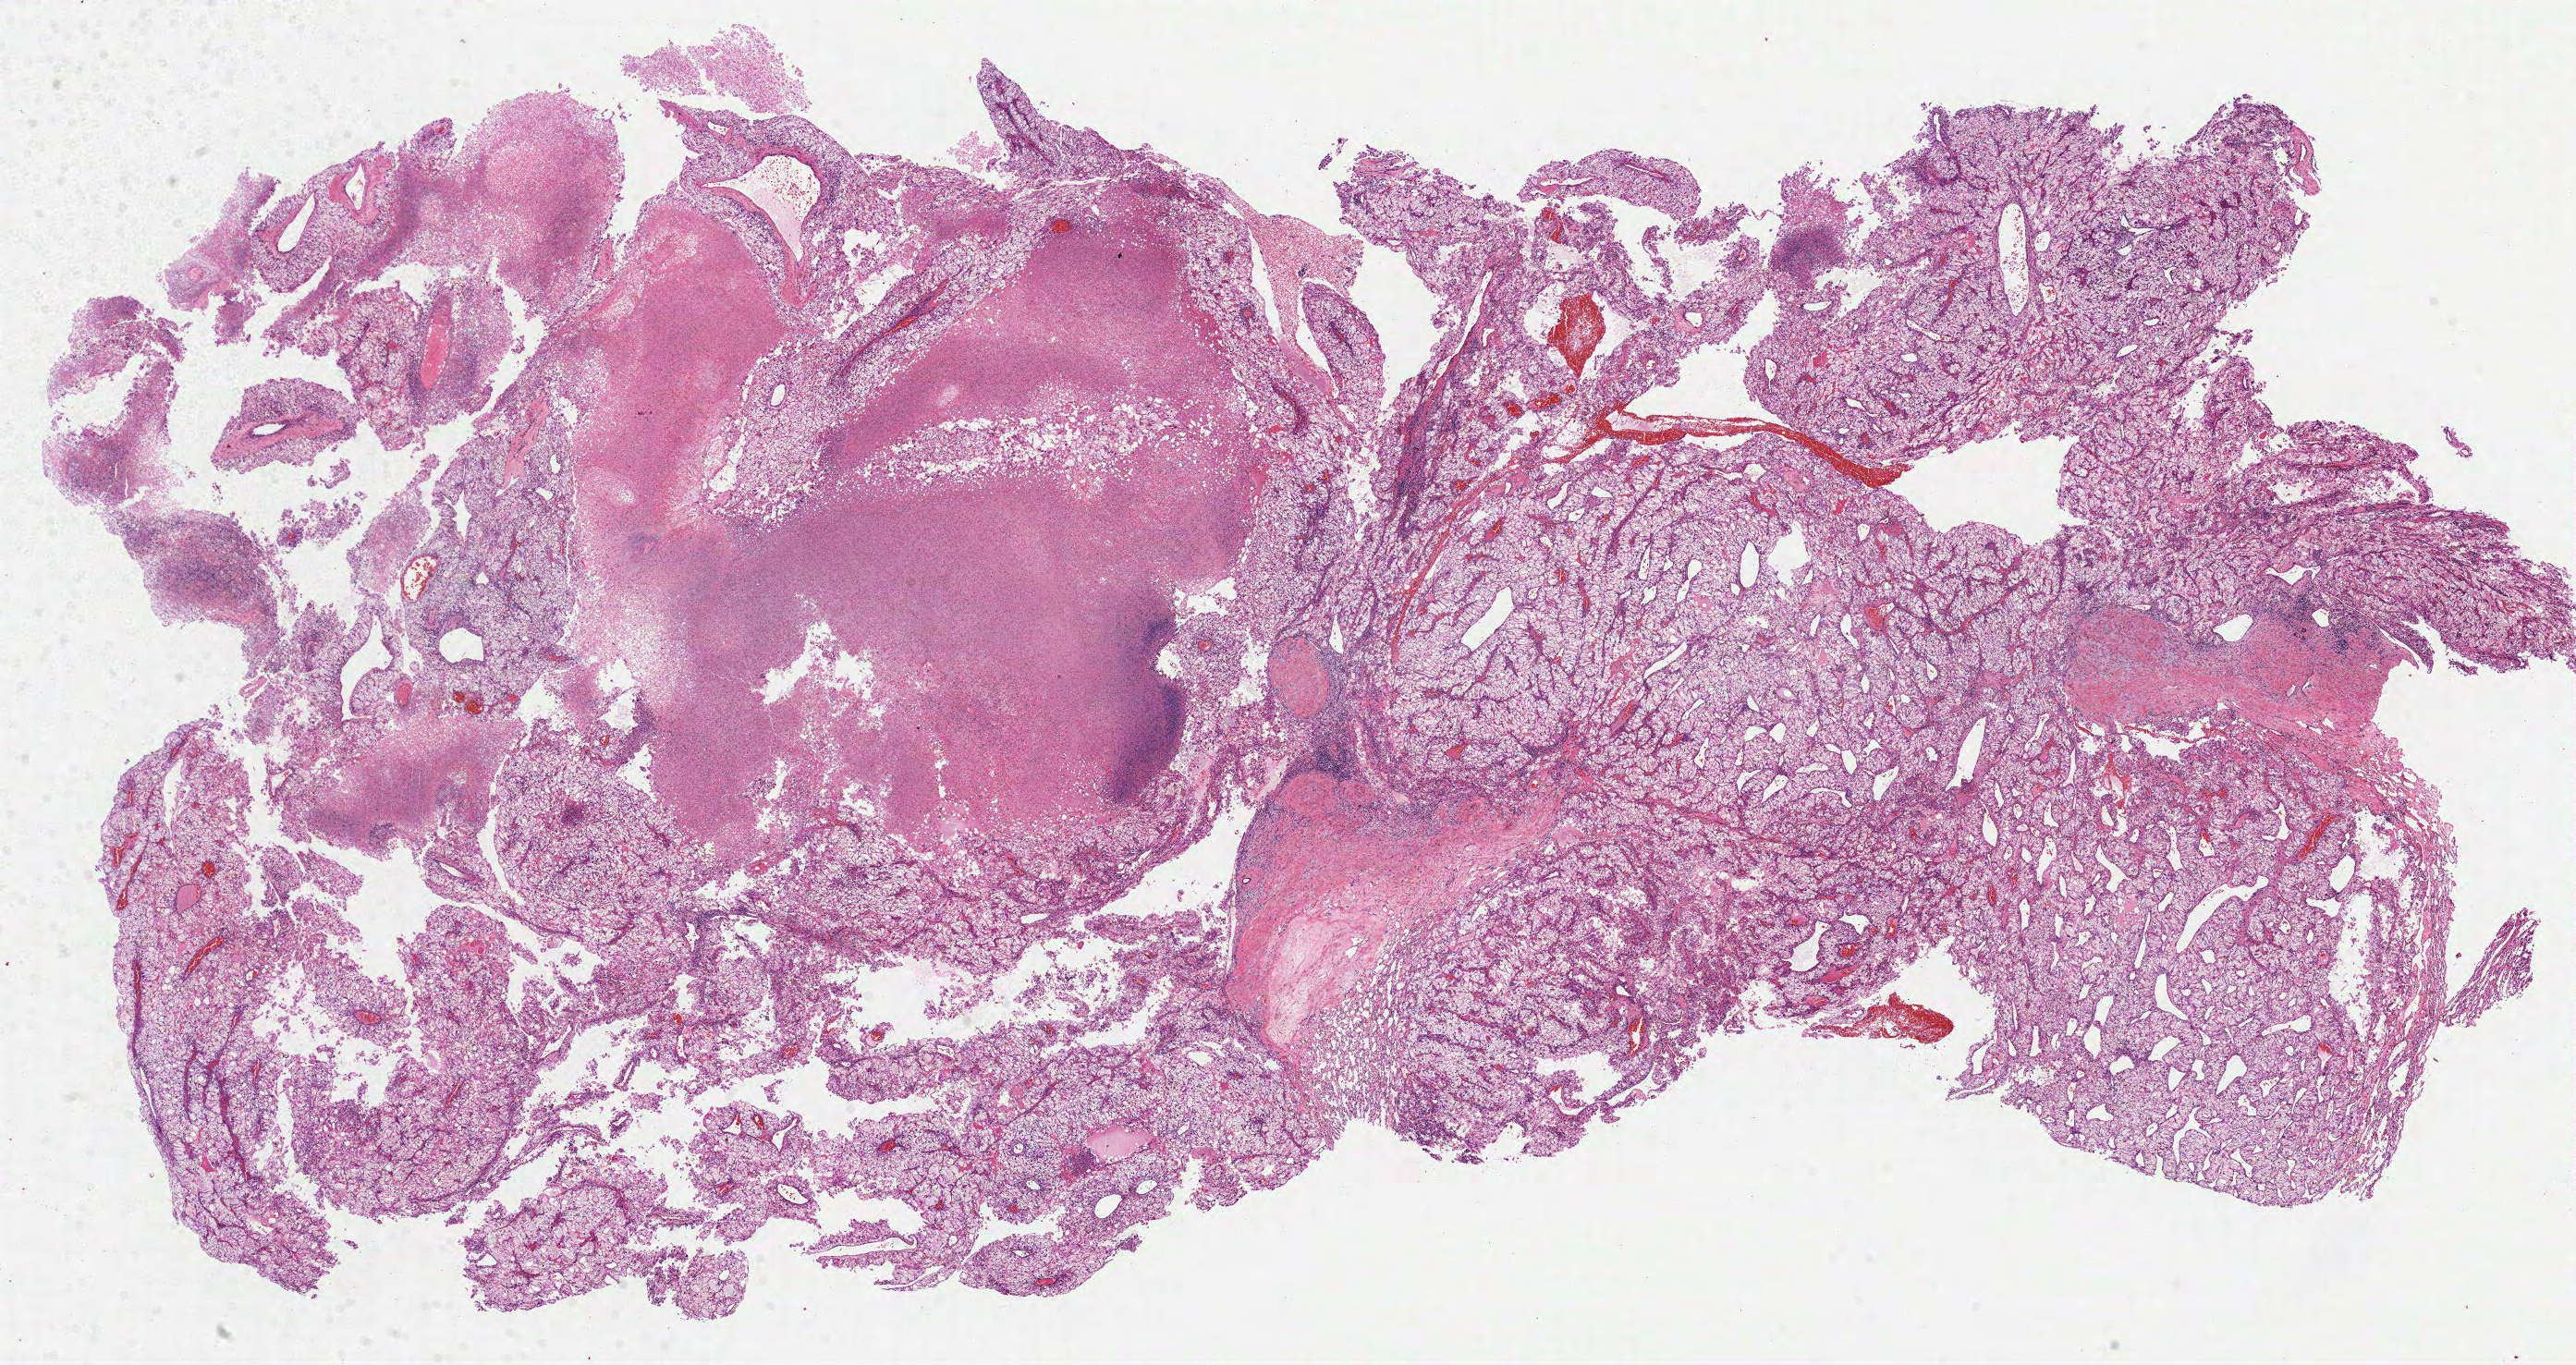
Whole-slide histology image, H&E — low-resolution overview of the scanned area, about 22.5 x 11.9 mm; formalin-fixed paraffin-embedded (FFPE) diagnostic section; primary tumour sample from the kidney. Male, age 65 years at initial diagnosis. Histologic grade: G2 (moderately differentiated).
AJCC pathologic stage: III. Diagnosis: Clear cell adenocarcinoma, NOS. Laterality: left.